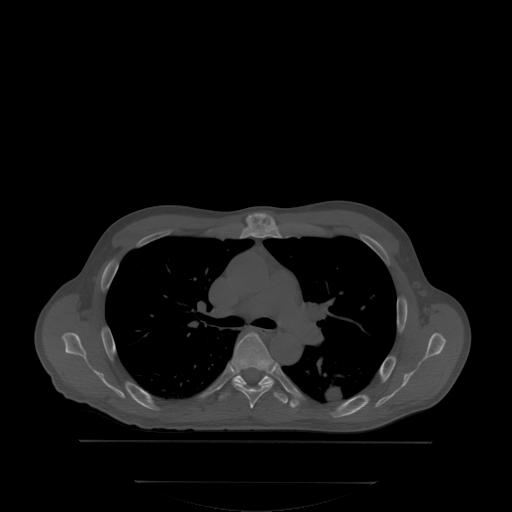
CT including the spine, one axial slice. Position 244 of 350 along the scan axis. Bone window (W 1800 / L 400 HU). 2.5 mm slice thickness. 512 × 512 image matrix, field of view 500 × 500 mm. Male patient, age 58 years. From the clinical record (not read from this slice): primary cancer: prostate.
Annotated regions visible in this slice (semi-automatically segmented with operator editing):
- T5 vertebra: box from (x=233, y=333) to (x=288, y=408) px
- T6 vertebra: (x=219, y=375)–(x=293, y=402)